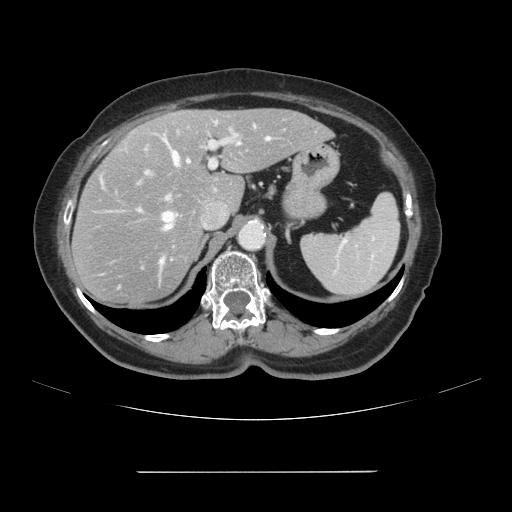
Contrast-enhanced abdominal CT, one axial slice. Slice 69 of 111 in the series (ordered by position). Intravenous contrast given. Soft-tissue window (W 400 / L 40 HU). 2.5 mm slice thickness. 512 × 512 image matrix, field of view 400 × 400 mm. Female patient, age 74 years. Case-level facts recorded for this patient, not image findings: diagnosis: colorectal cancer liver metastases, imaged before liver resection; multiple liver metastases: yes; largest metastasis: 1.1 cm; disease in both lobes: yes.
Structures marked on this image (expert manual segmentation):
- hepatic veins: box from (x=101, y=137) to (x=271, y=290) px
- liver: (x=74, y=109)–(x=331, y=306)
- planned liver remnant (the part of the liver to remain after resection): (x=151, y=109)–(x=331, y=210)
- portal vein (with intrahepatic branches): (x=146, y=122)–(x=237, y=201)